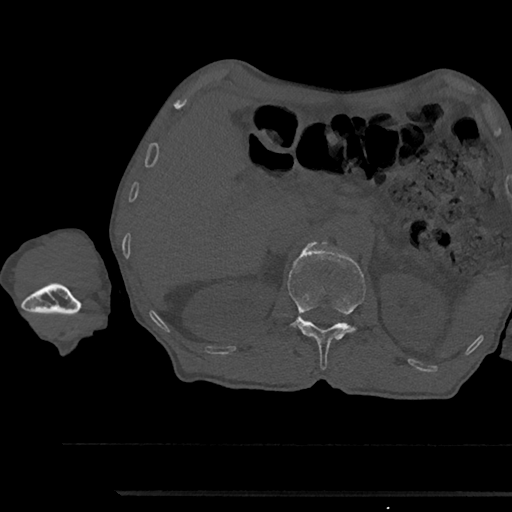
CT including the spine, one axial slice. Position 634 of 797 along the scan axis. Bone window (W 1800 / L 400 HU). 0.5 mm slice thickness. 512 × 512 image matrix. Male patient, age 79 years. From the clinical record (not read from this slice): primary cancer: prostate.
Structures marked on this image (semi-automatically segmented with operator editing):
- L1 vertebra: bounding box [x1, y1, x2, y2] px = [287, 243, 366, 370]